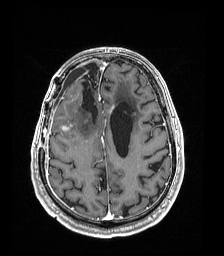
Brain MRI from a brain-tumour surgery series, one axial slice; slice 59 of 192 in the series (ordered by position); T1-weighted post-contrast; 1 mm slice thickness; 224 × 256 image matrix. From the clinical record (not read from this slice): histopathology: Astrocytoma; WHO grade: 4; IDH mutation: yes; tumour location: Right Frontal.
Structures marked on this image (manually delineated by an expert):
- previous resection cavity: bounding box [x1, y1, x2, y2] px = [81, 68, 98, 122]